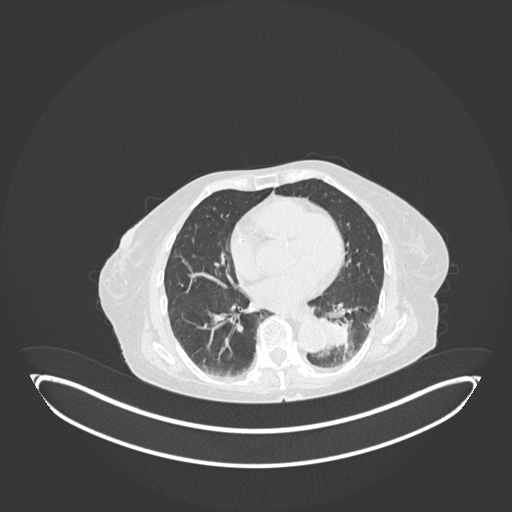
Chest CT, one axial slice; position 45 of 189 along the scan axis; reconstruction kernel B30f; 120 kVp; lung window (W 1500 / L -600 HU); 1 mm slice thickness; 512 × 512 image matrix, field of view 500 × 500 mm. Patient: female, 82 years. From the clinical record (not read from this slice): clinical TNM (as recorded): T1b N0 M1.
Structures marked on this image (rectangle marked by the reading radiologist):
- lung tumour (recorded histology: adenocarcinoma): bounding box (x1, y1, x2, y2) in pixels: (313, 311, 354, 352)